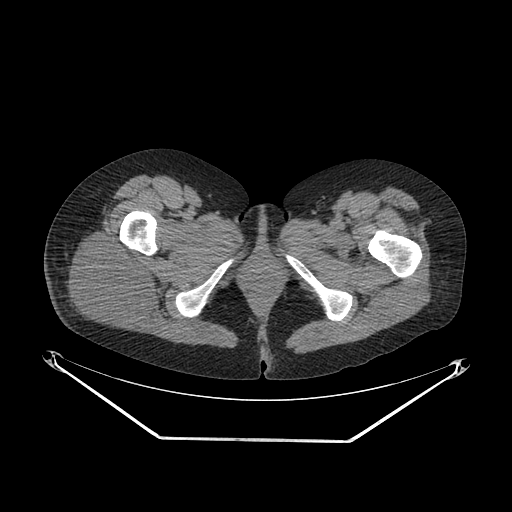
CT of an extremity soft-tissue mass (from a PET/CT study), one axial slice; slice 35 of 267 in the series (ordered by position); reconstruction kernel SOFT; 140 kVp; soft-tissue window (W 400 / L 40 HU); 3.75 mm slice thickness; 512 × 512 image matrix. Female patient. From the clinical record (not read from this slice): histological type: epithelioid sarcoma with vascular differentiation; site of the primary tumour: right buttock.
Outlined on this slice (expert contour drawn on MRI and transferred to this co-registered scan by the dataset authors):
- gross tumour volume (mass): bounding box [x1, y1, x2, y2] px = [66, 235, 152, 328]